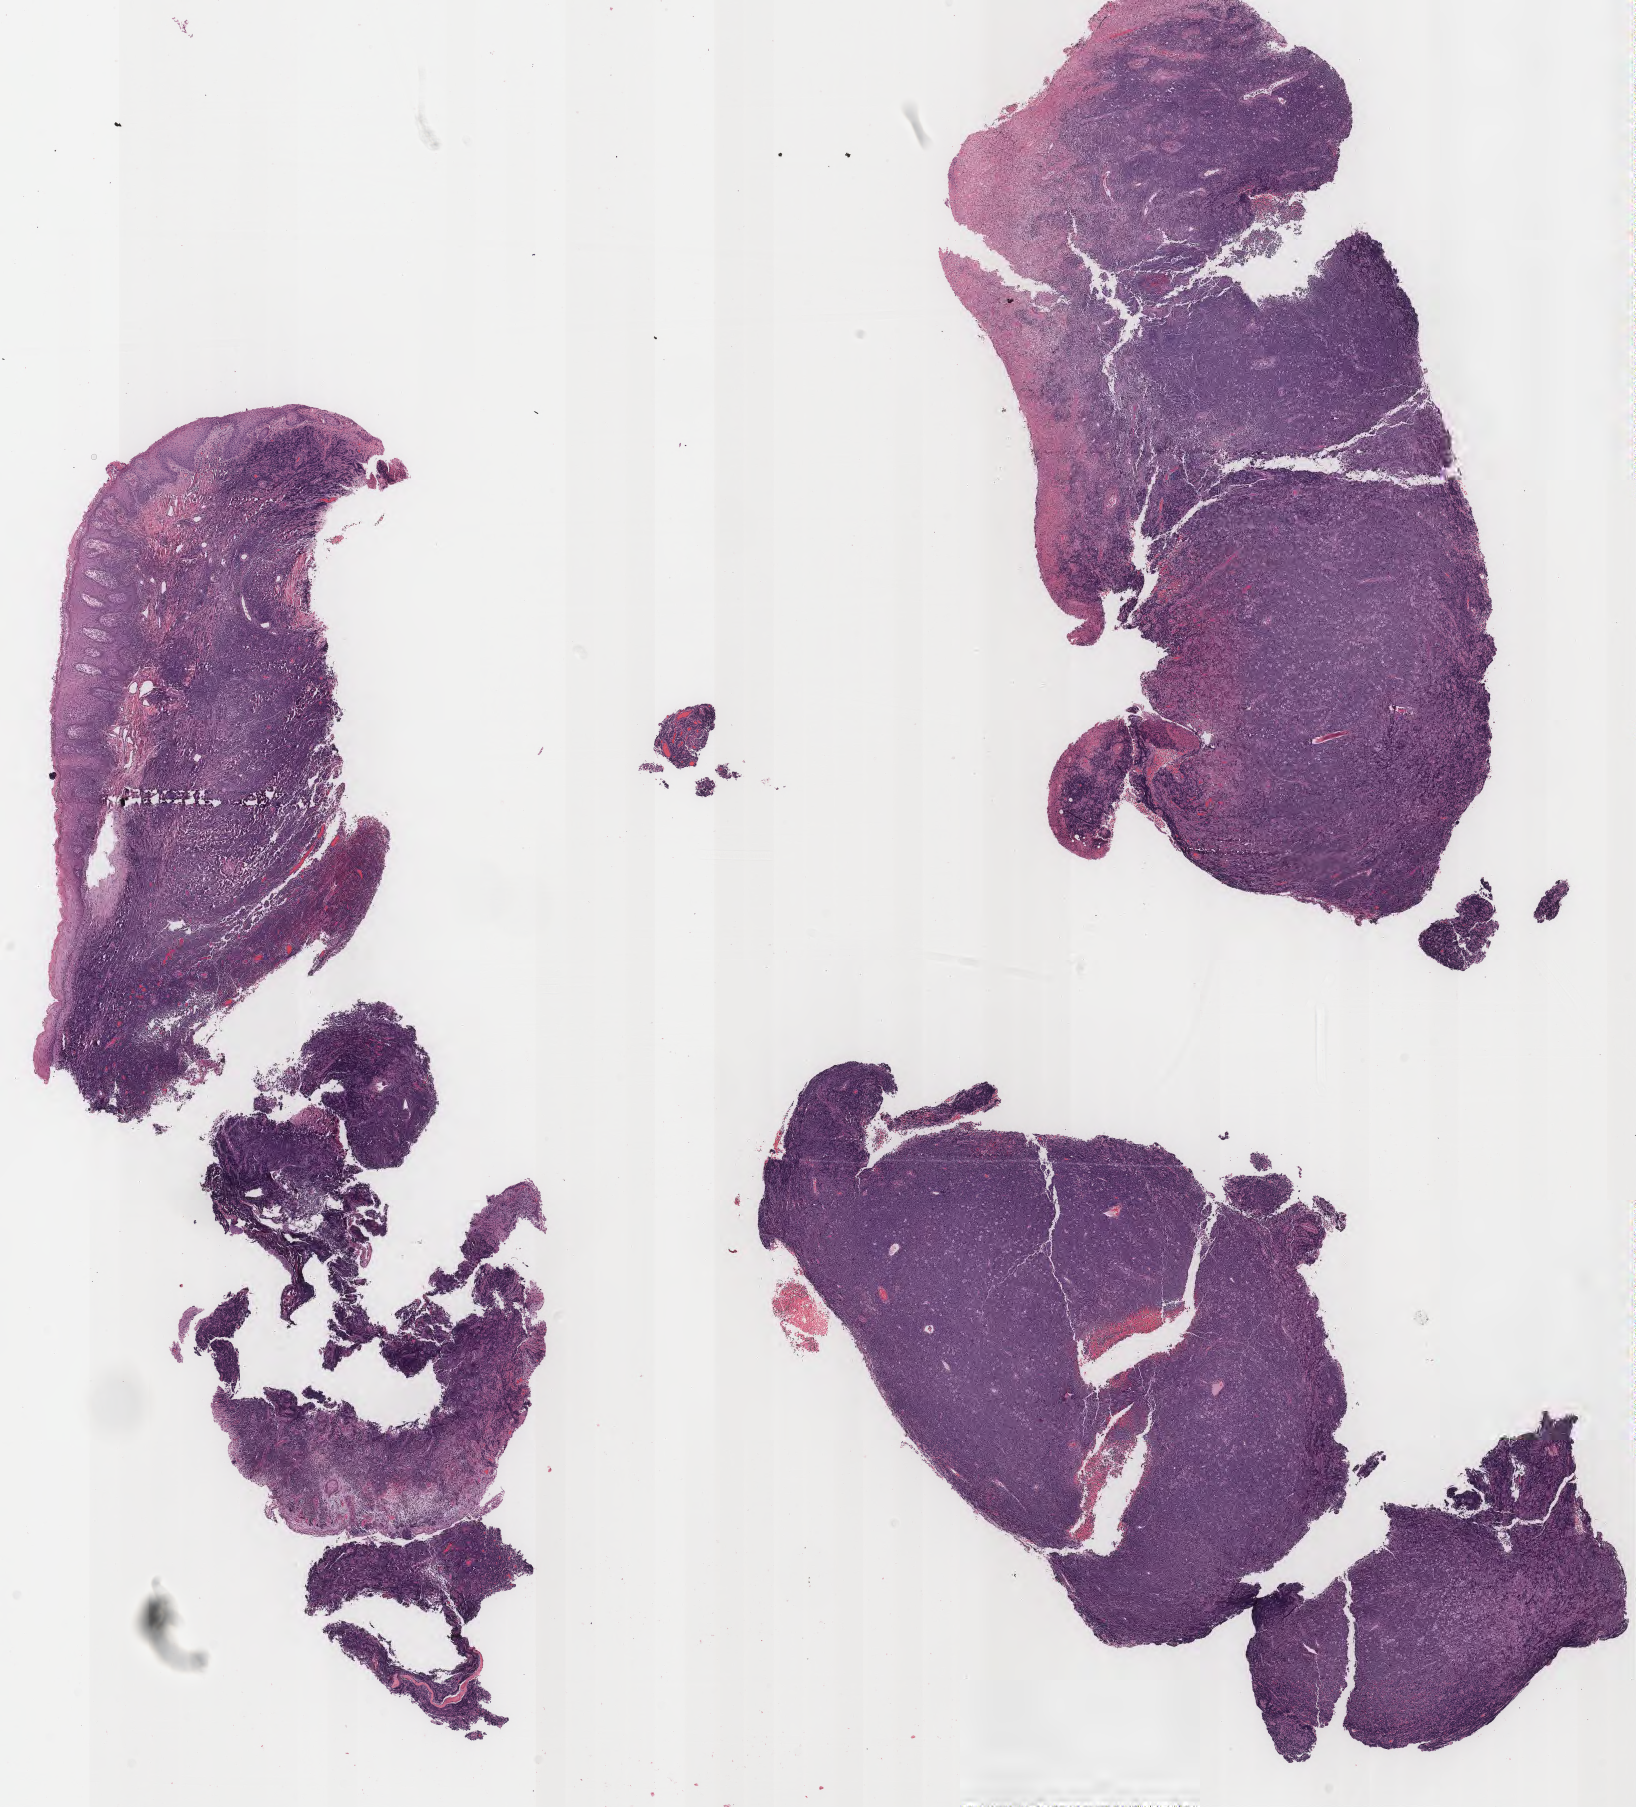
Digitized hematoxylin and eosin (H&E)-stained section — low-resolution overview of the scanned area, about 13.0 x 14.3 mm. Specimen: tumor tissue. Patient: male, aged 22.
* histologic diagnosis: Burkitt lymphoma, NOS